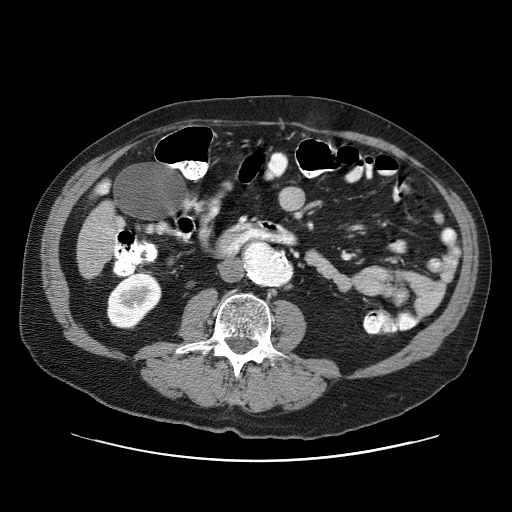
Contrast-enhanced abdominal CT (liver protocol), one axial slice. Slice 5 of 87 in the series (ordered by position). Reconstruction kernel STANDARD. One of 3 acquisitions stored at this slice position. Soft-tissue window (W 400 / L 40 HU). 512 × 512 image matrix, field of view 400 × 400 mm. From the clinical record (not read from this slice): diagnosis: hepatocellular carcinoma (patient treated with transarterial chemoembolisation; whether this scan precedes or follows treatment is not stated here); TNM stage (as recorded): Stage-IIIA; Child-Pugh class: A; tumour size: 6 cm.
Structures marked on this image (semi-automatic segmentation, software-assisted and operator-edited):
- liver parenchyma outside the tumour (the mass and vessels are separate outlines, so this box may not span the whole liver): bounding box (x1, y1, x2, y2) in pixels: (76, 181, 123, 278)
- liver vessels: (101, 185, 112, 234)